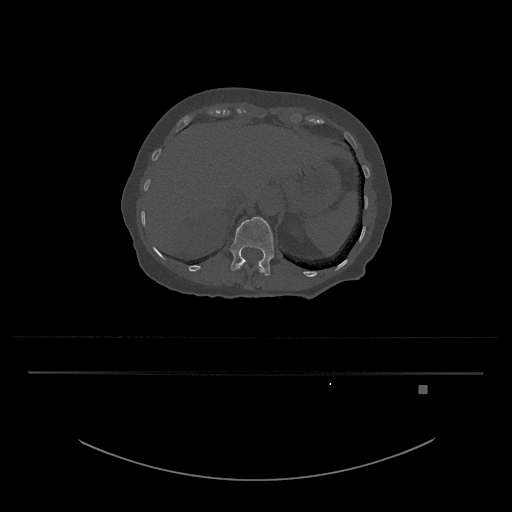
CT including the spine, one axial slice; slice 573 of 797 in the series (ordered by position); reconstruction kernel Br40s/3; bone window (W 1800 / L 400 HU); 512 × 512 image matrix, field of view 500 × 500 mm. Female patient, age 57 years. Case-level facts recorded for this patient, not image findings: primary cancer: cervical.
Annotated regions visible in this slice (semi-automatic segmentation, software-assisted and operator-edited):
- L1 vertebra: bounding box <230,217,274,276> (left, top, right, bottom; pixels)
- T12 vertebra: <236,262,264,273>